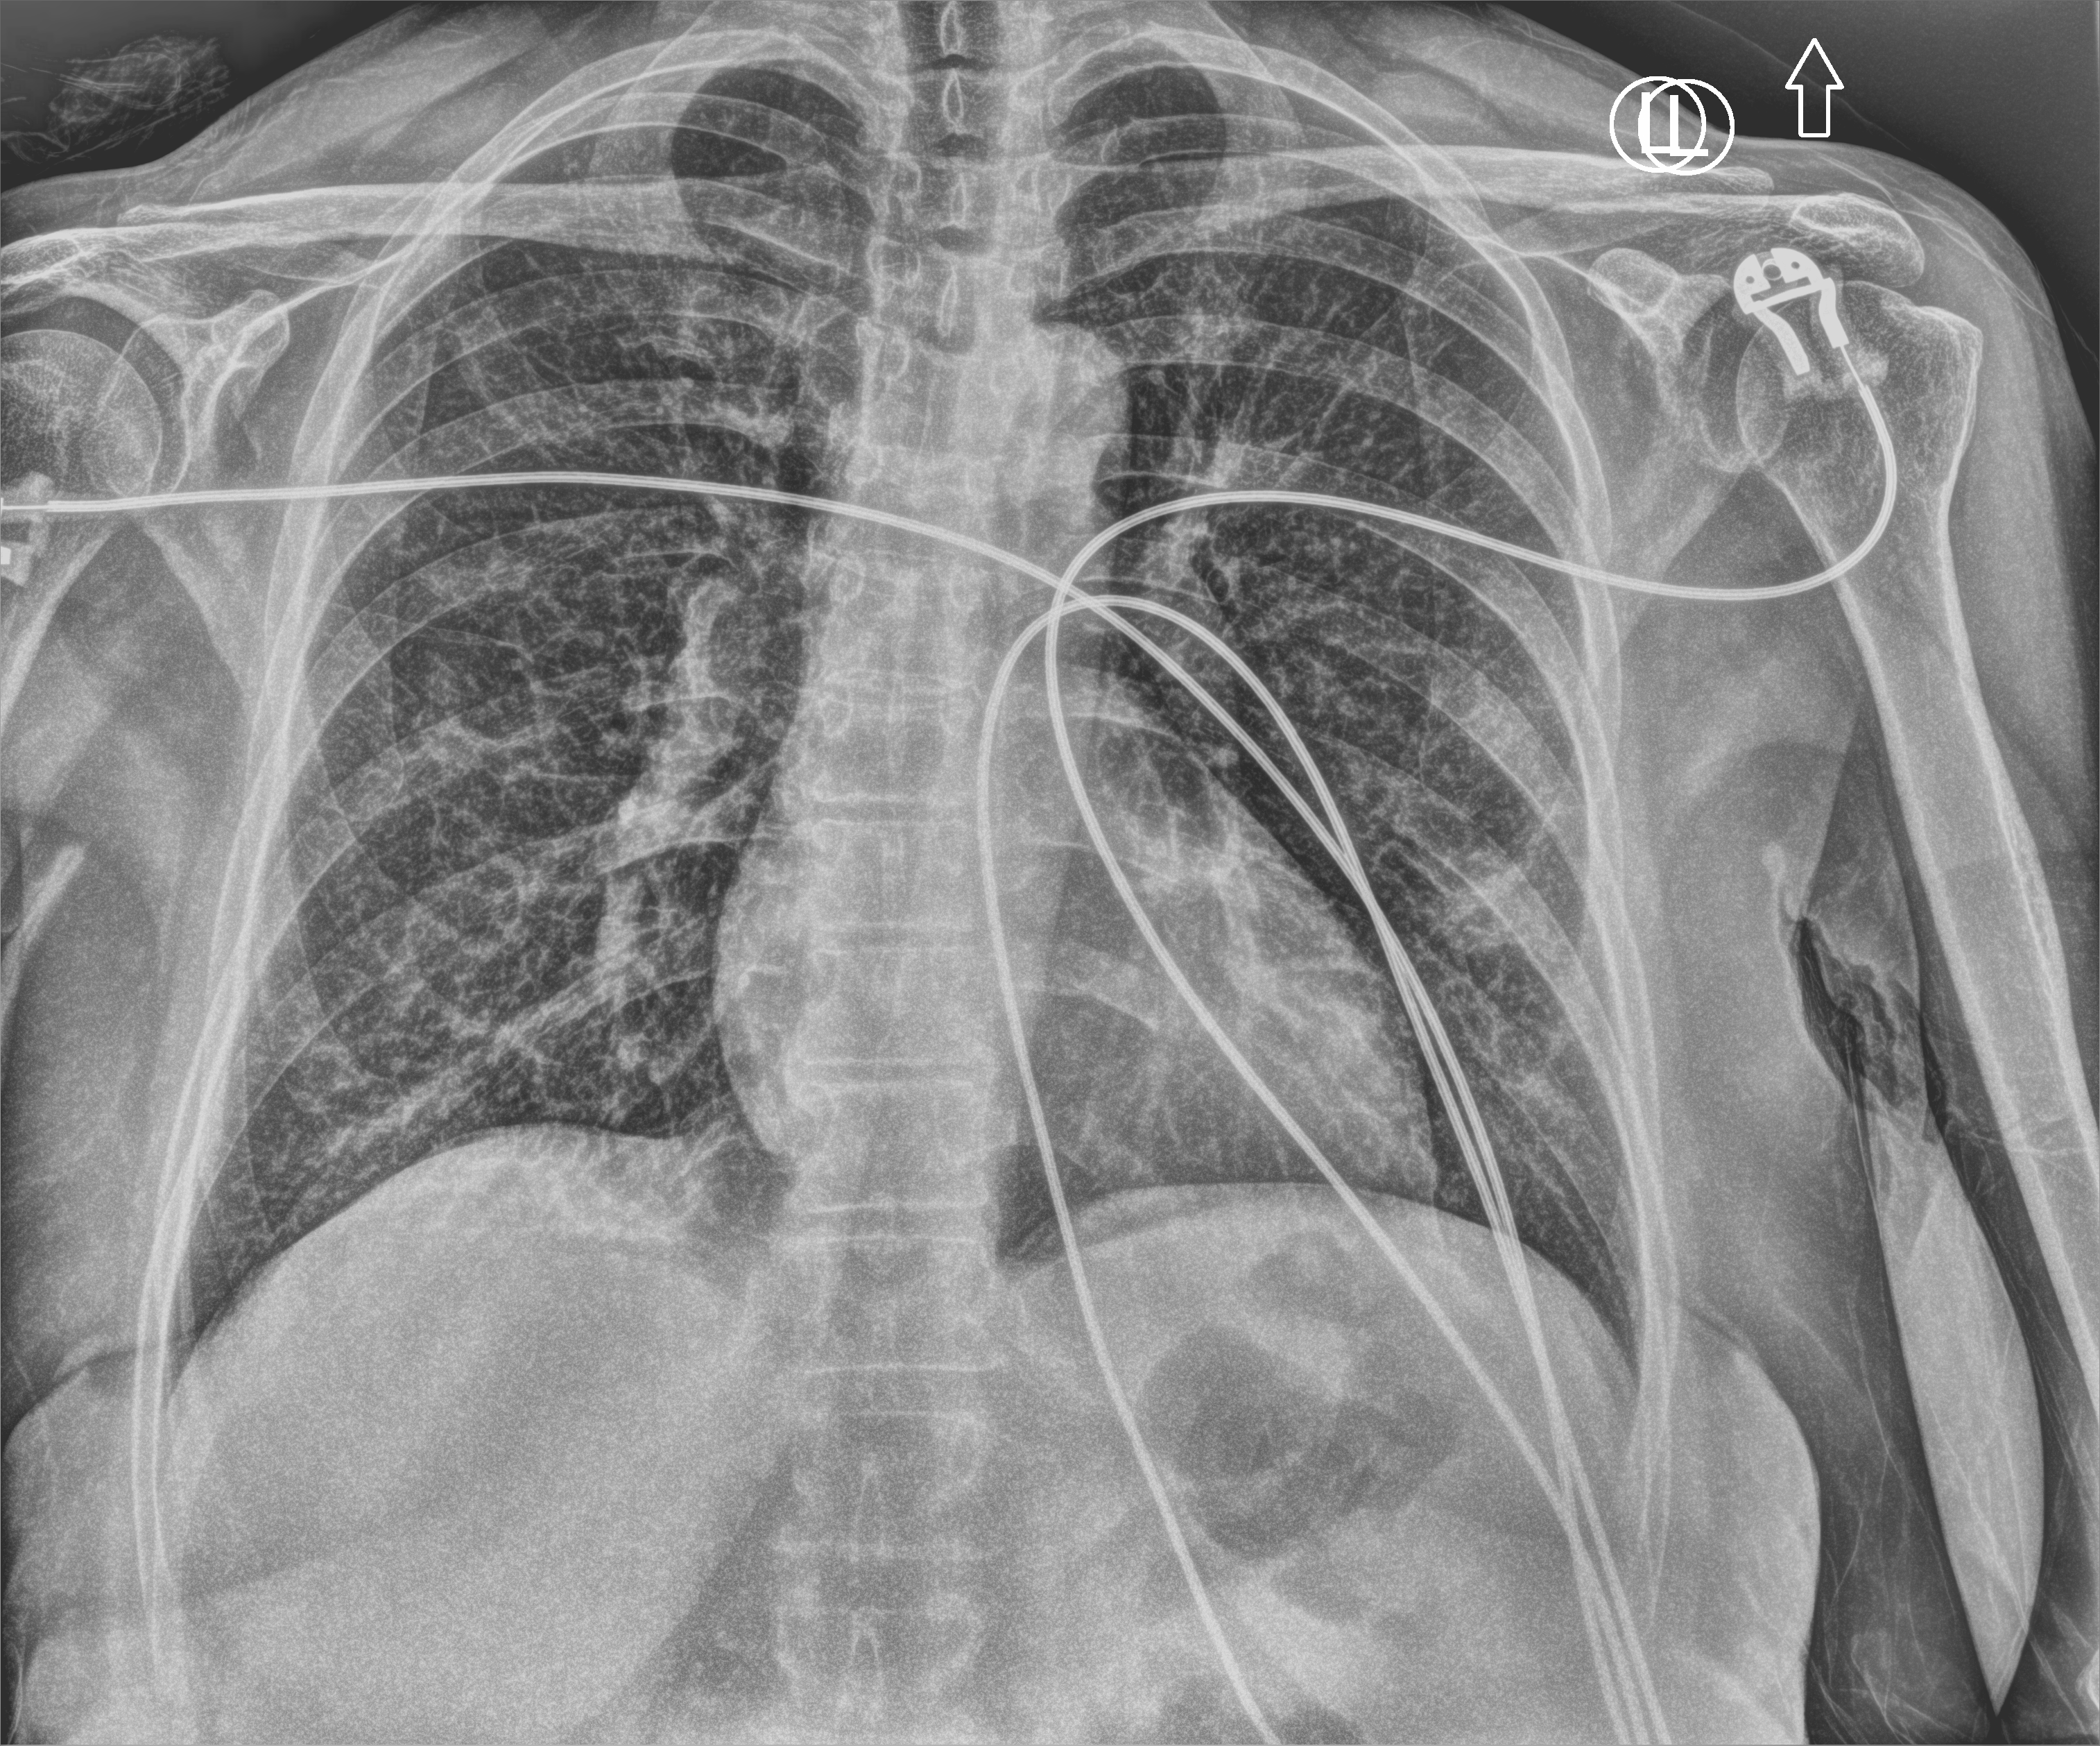
Chest X-ray (portable); anteroposterior (AP) projection. Patient hospitalised with COVID-19; female, aged 60–74 years.
Admission-level facts for this patient (not findings on this image; timing relative to this image not recorded):
- admitted to intensive care during this hospital stay: no